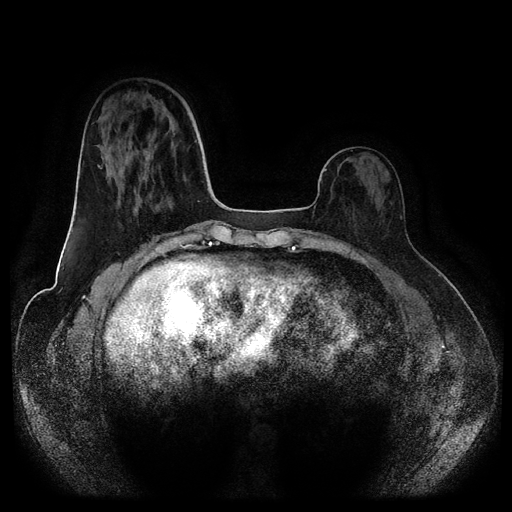
Breast MRI (dynamic contrast-enhanced, multi-phase), one axial slice. Position 34 of 116 along the scan axis. Dynamic contrast-enhanced series, time point 2 of 5 at this slice position (early post-contrast). 1.5 T. TE 2.6 ms, TR 5.2 ms. 2 mm slice thickness. 512 × 512 image matrix, field of view 380 × 380 mm. Female patient, age 50 years.
Annotated regions visible in this slice (semi-automatic segmentation, software-assisted and operator-edited):
- breast lesion (labelled benign in the annotation): bounding box (x1, y1, x2, y2) in pixels: (144, 144, 151, 161)